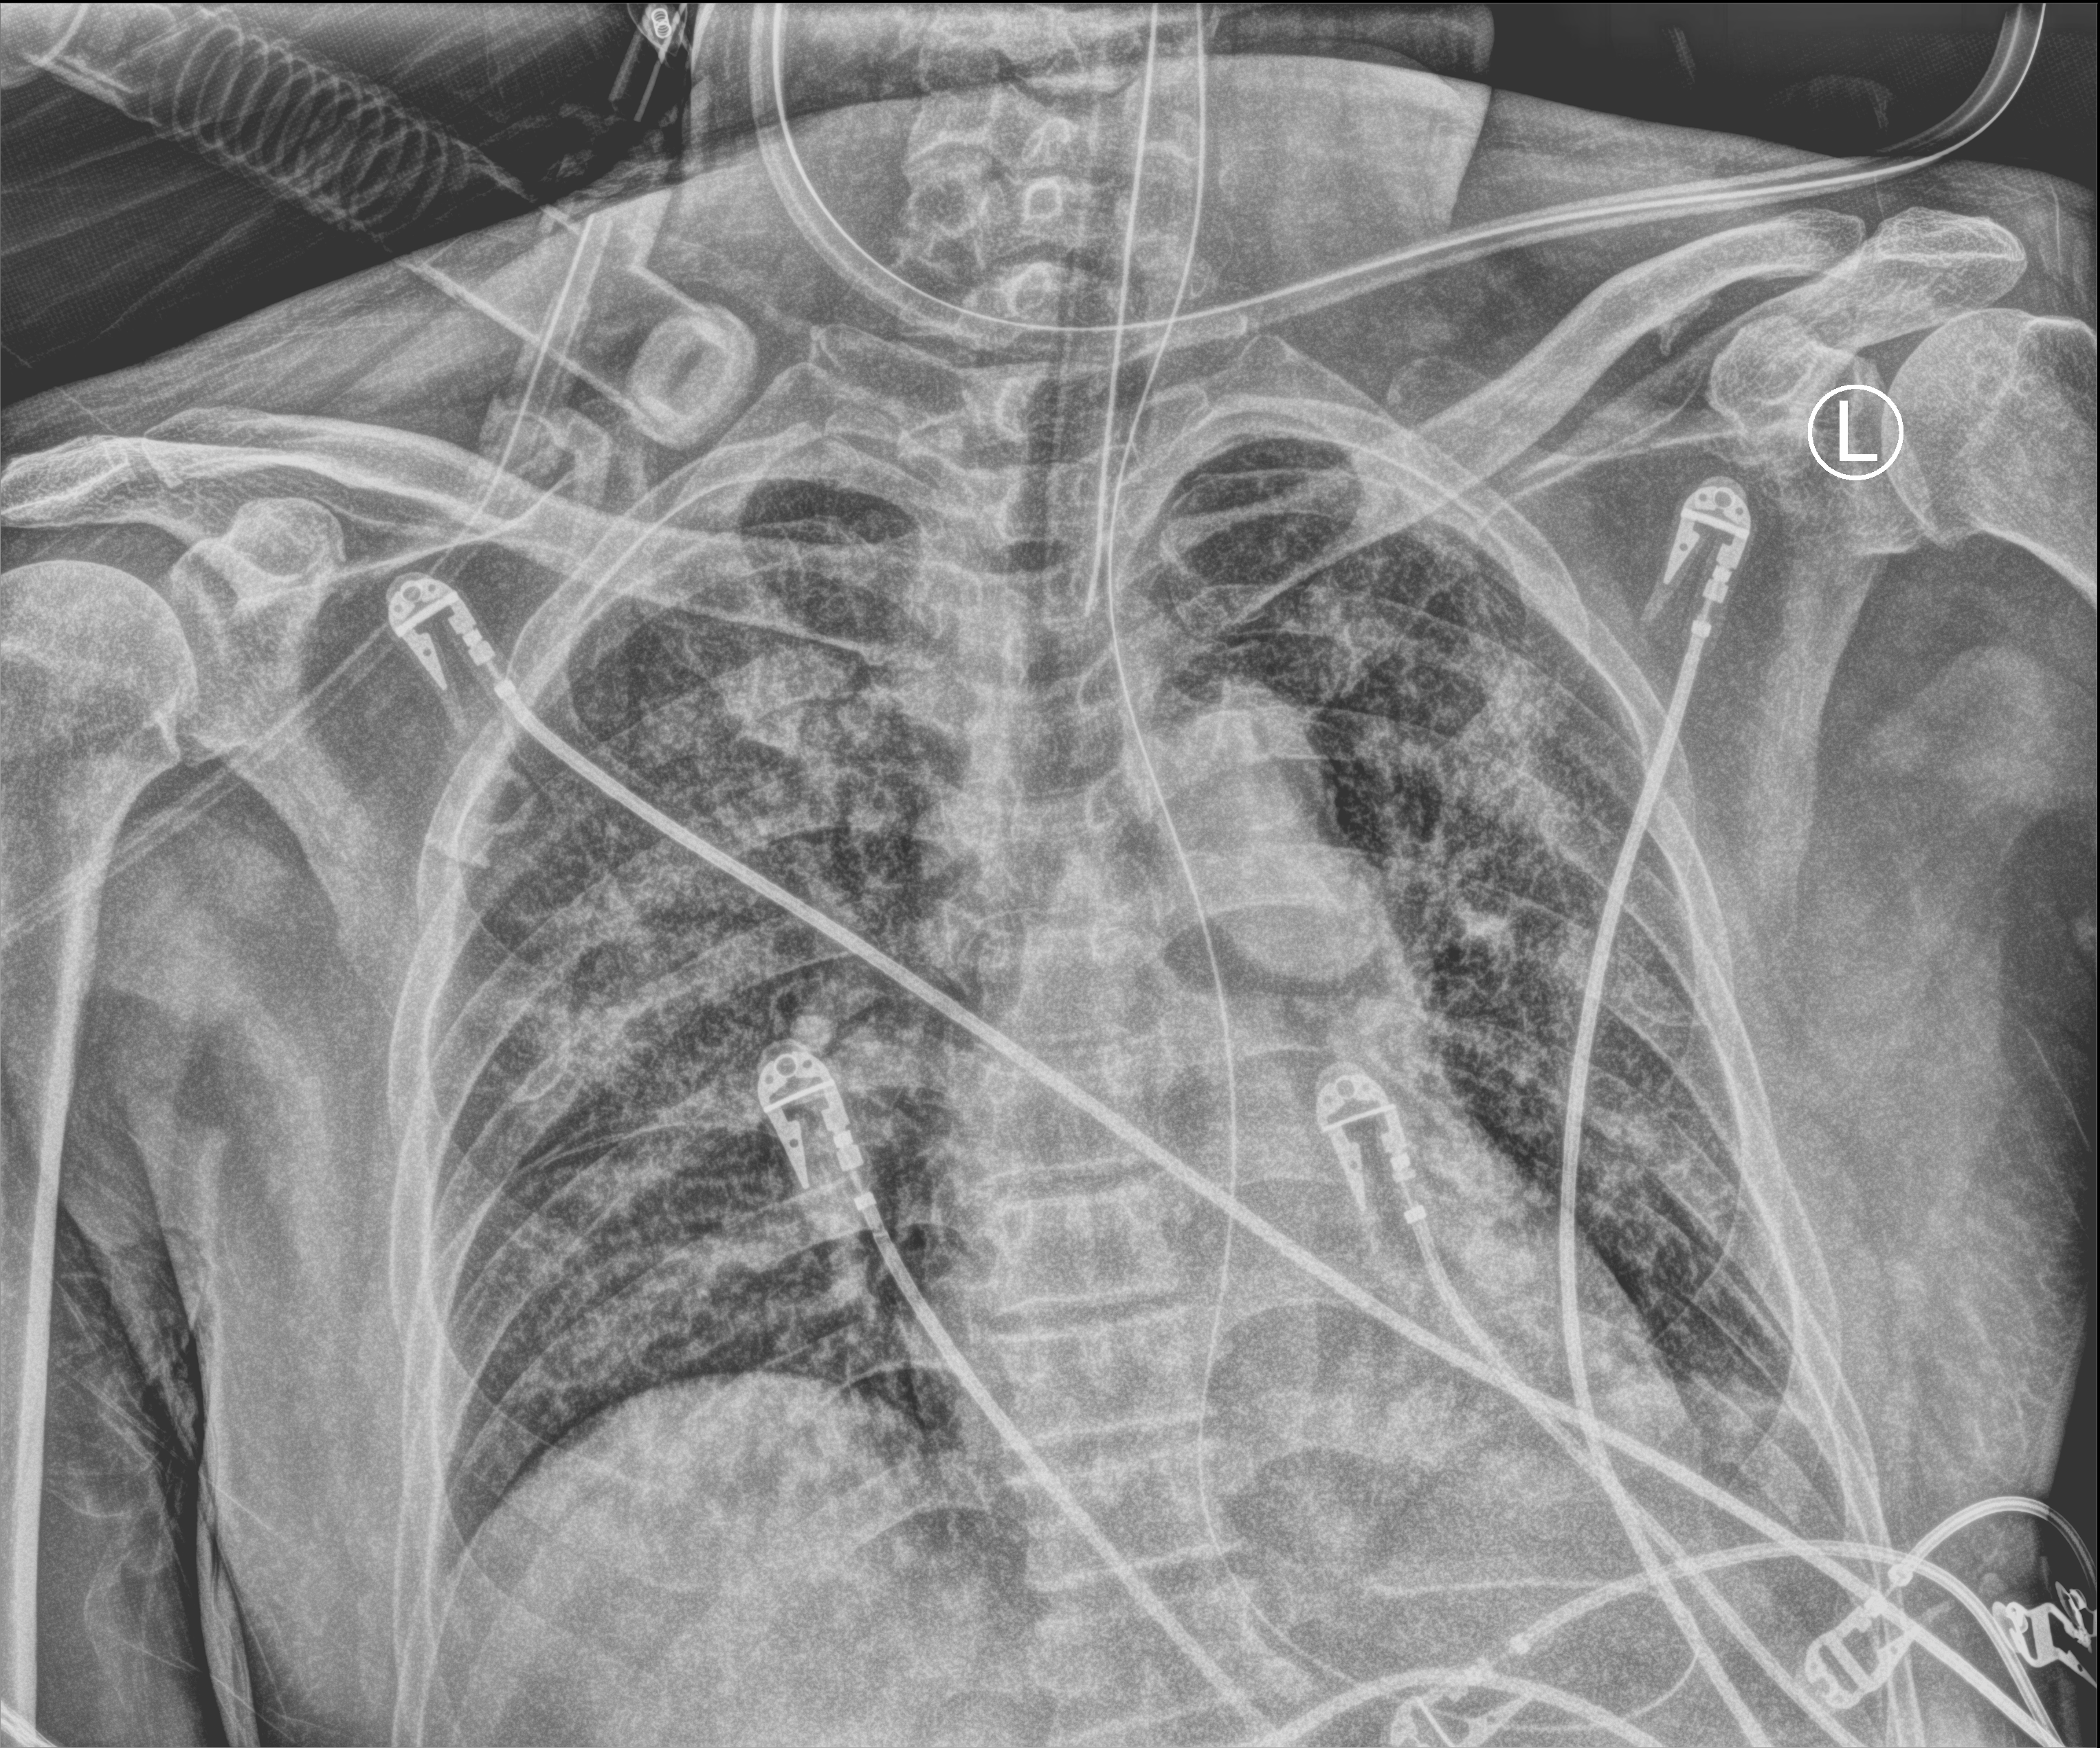
Bedside chest radiograph (computed radiography), anteroposterior (AP) projection. Patient hospitalised with COVID-19; male, aged 60–74 years.
Hospital-stay facts (about this admission, not read from this image; timing relative to this image not recorded):
- diabetes (admission record): yes
- mechanically ventilated during this hospital stay: yes
- admitted to intensive care during this hospital stay: yes